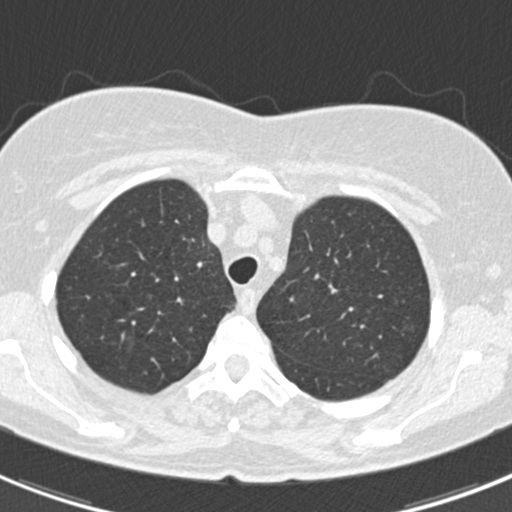
Axial slice from a low-dose chest CT screening exam; first (baseline) screen; lung window (W 1500 / L -600 HU); slice 44 of 184 in the series. Female, age 60 years at enrolment.
Lesion marked by an expert reader, bounding box (x1, y1, x2, y2) in pixels: (384, 306, 424, 342). The screening reader recorded 3 non-calcified nodules or masses ≥4 mm on this exam (lingula, left lower lobe, lingula); which of them this box marks is not recorded. Official screen result: positive, change unspecified: nodule(s) >= 4 mm or enlarging nodule(s), mass(es), or other non-specific abnormalities suspicious for lung cancer. Participant outcome: lung cancer diagnosed 886 days after this screen (after the third annual screen) — non-small cell carcinoma, left upper lobe, poorly differentiated (G3), stage IB (AJCC 6th edition), 7 mm at pathology.